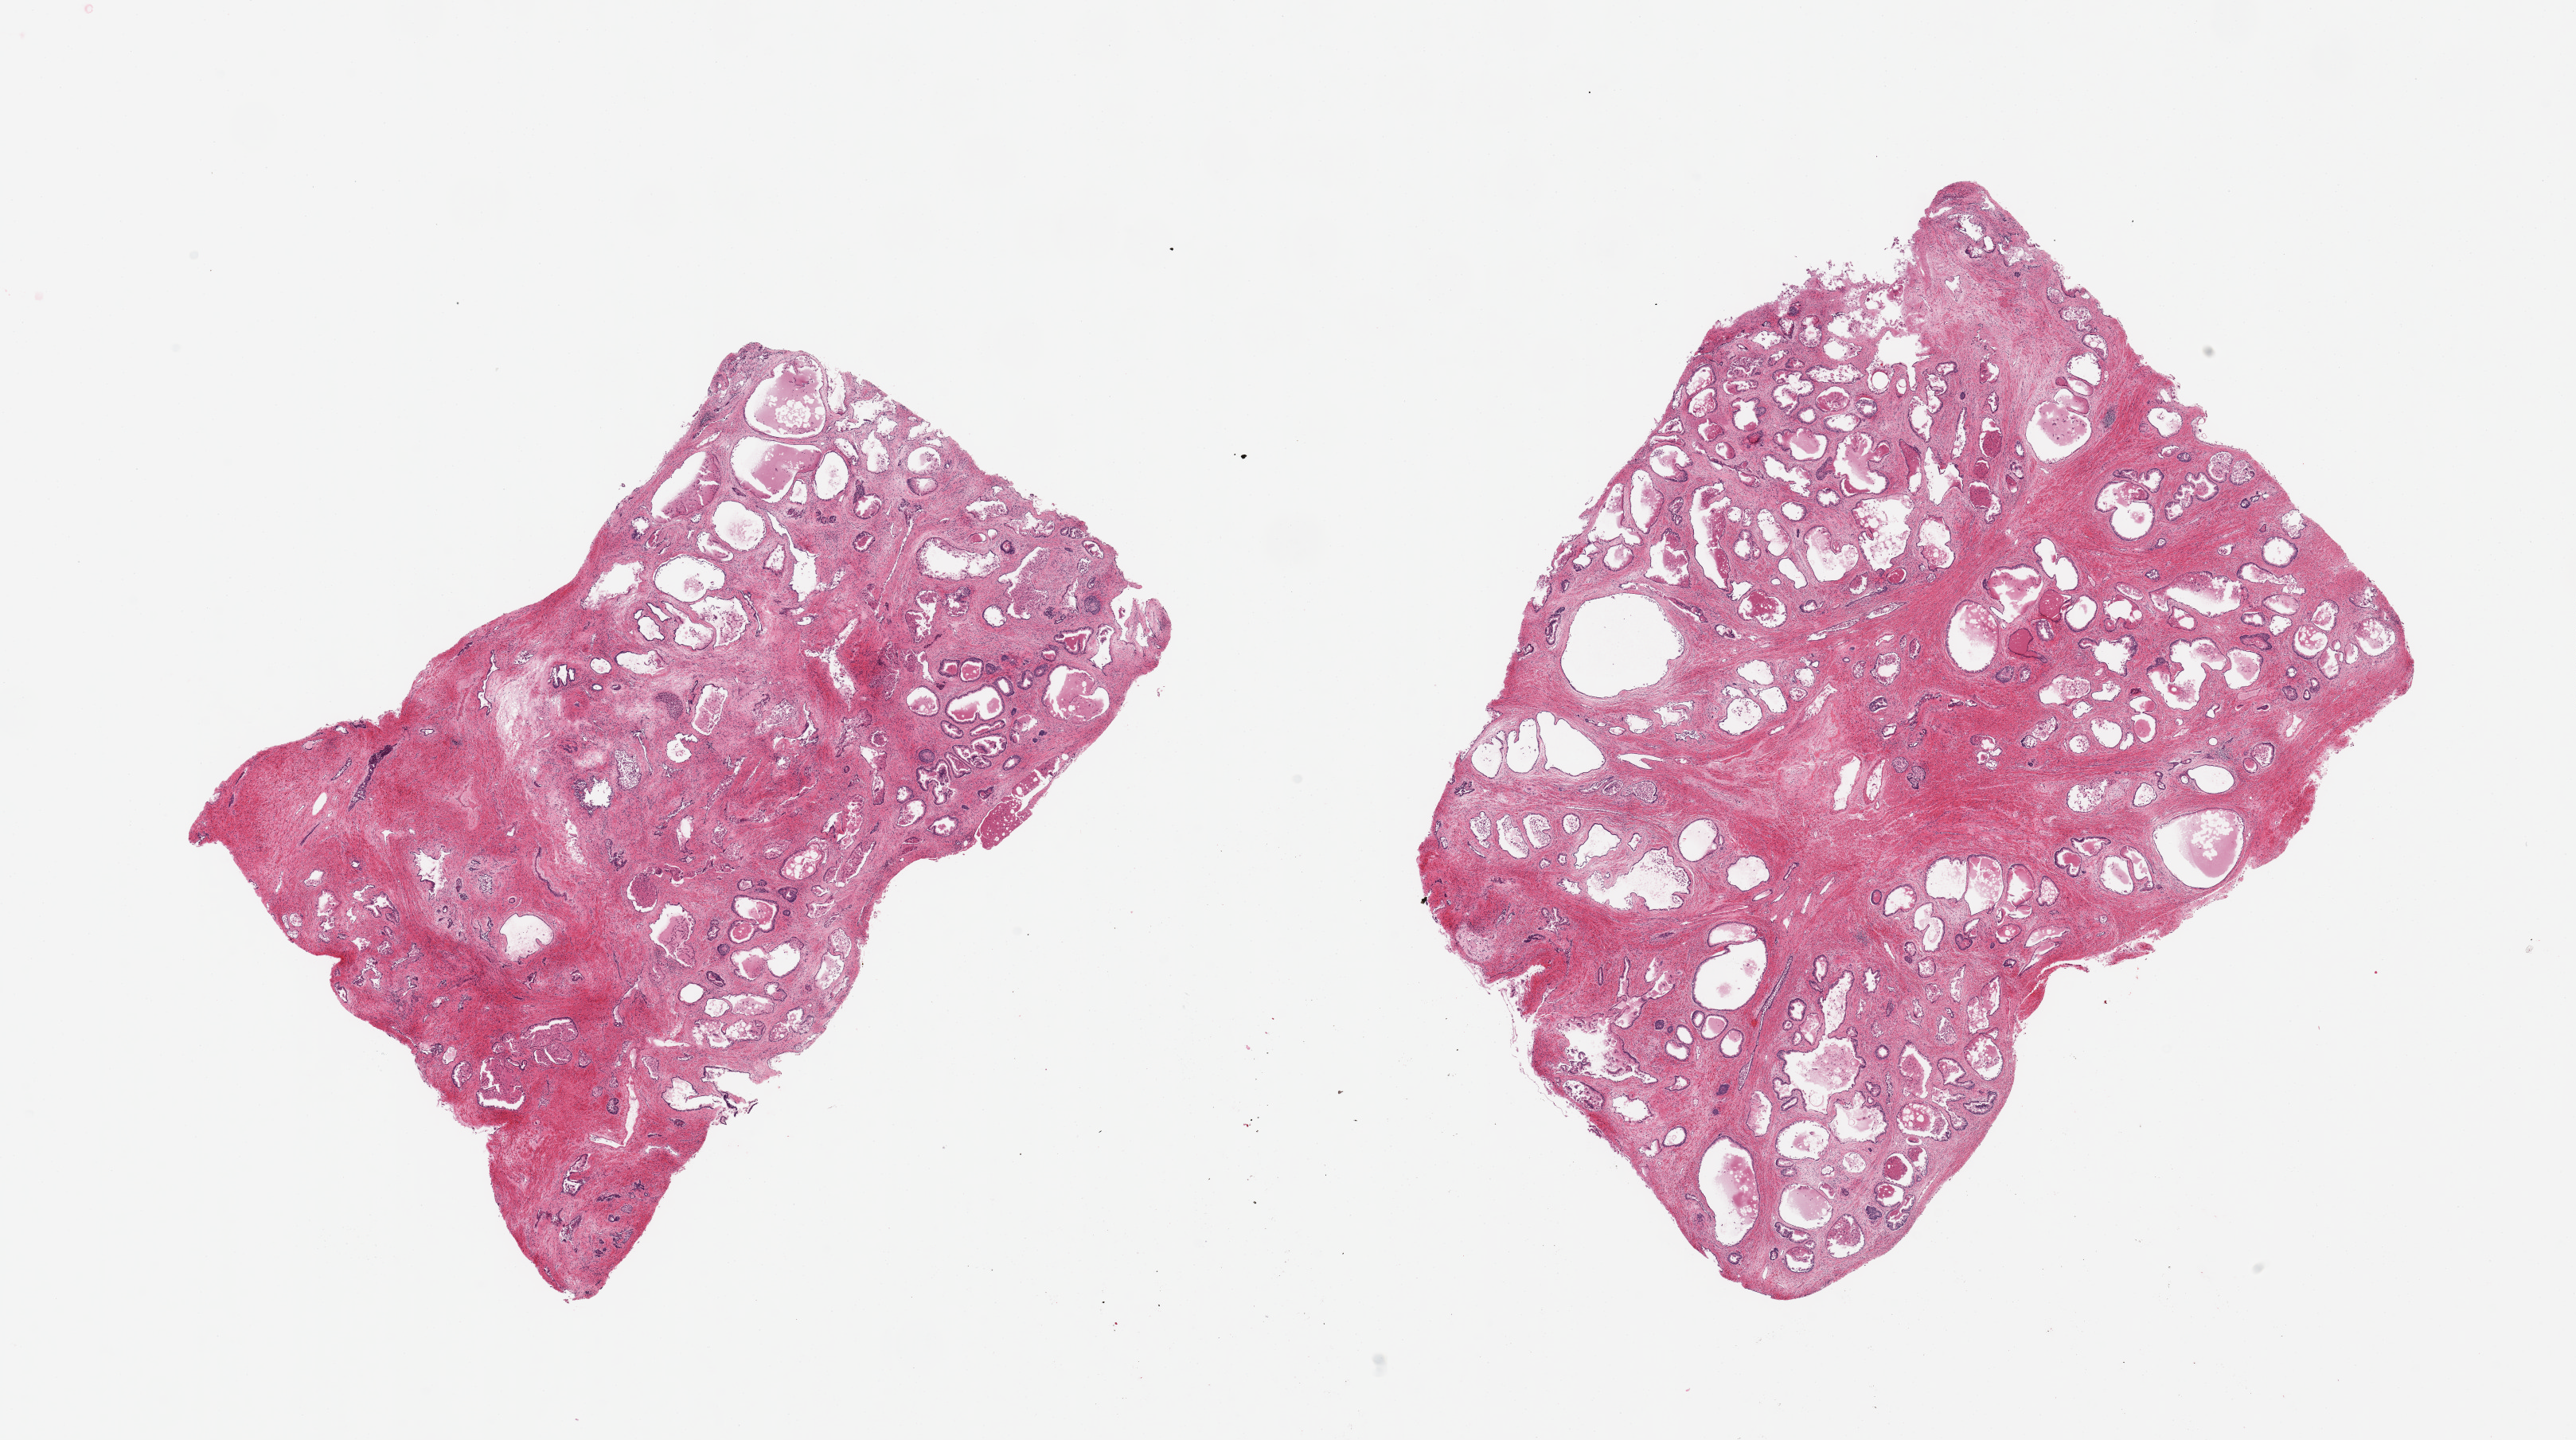
Whole-slide image, haematoxylin and eosin stain, brightfield — a low-resolution overview of the entire scanned area, about 25.6 x 14.3 mm (slide scanned at 20x). PAXgene-fixed, paraffin-embedded tissue. Sampled site (target tissue): prostate. Donor tissue sample. Donor: male.
Review note (as recorded): 2 pieces, glandular copmponent appears cystic, nodular/hyperplastic glandular pattern.